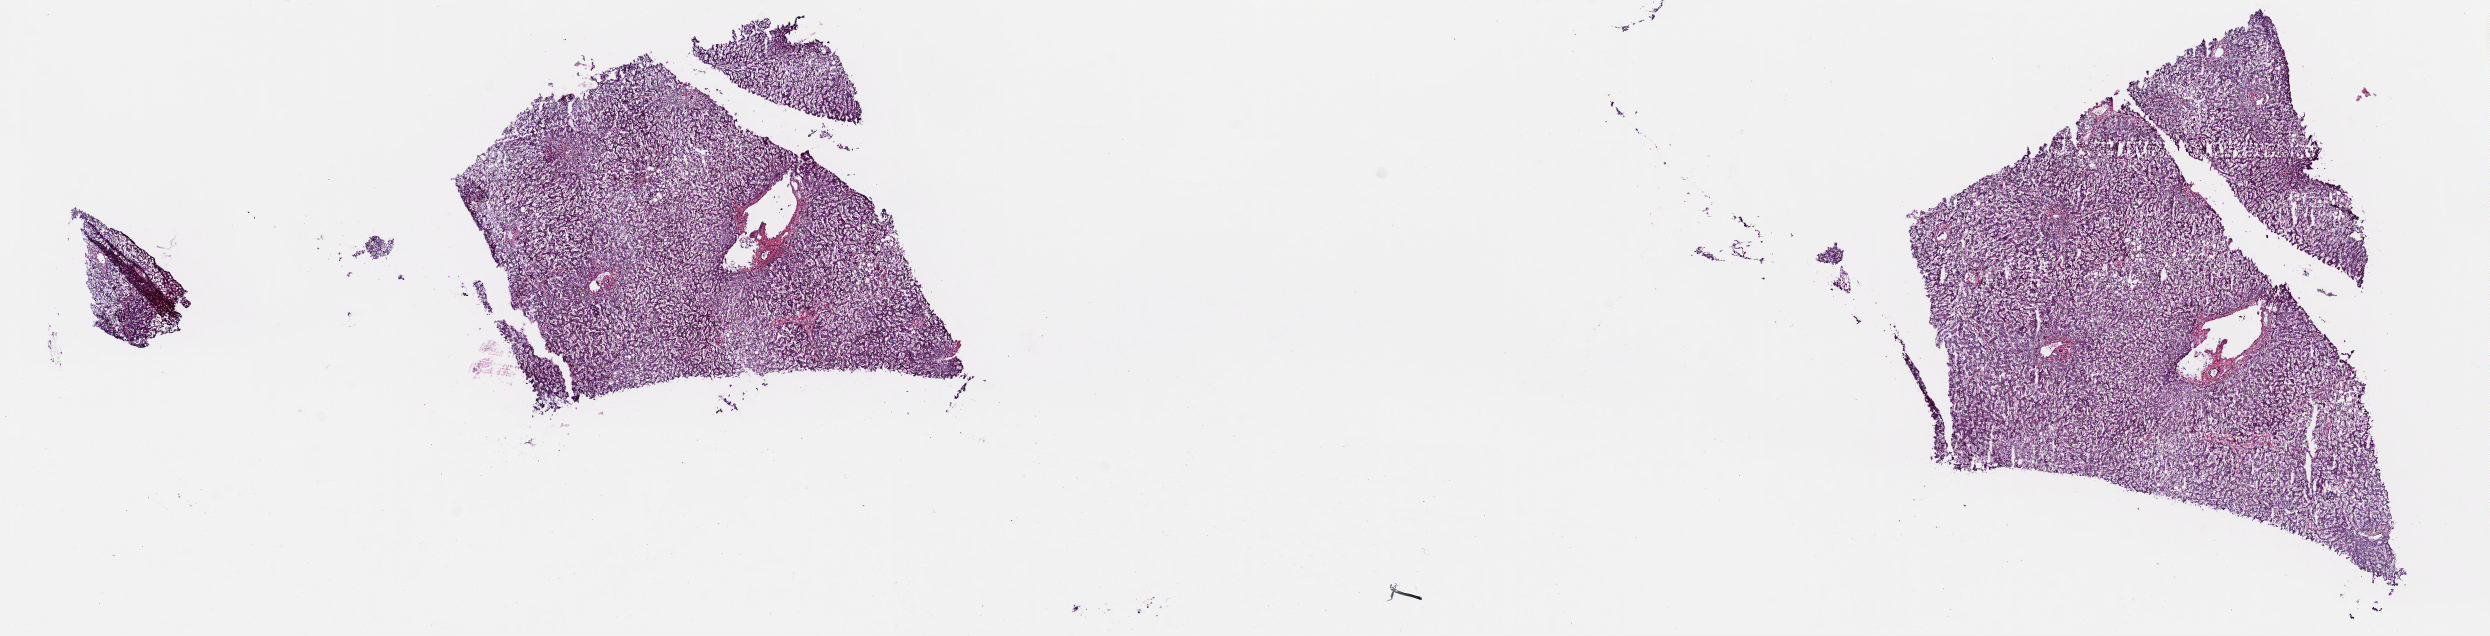
H&E whole-slide image — shown as a low-resolution overview of the whole scanned area (about 19.7 x 5.0 mm). Frozen section. Liver, solid tissue normal (non-tumour tissue) sample. Male, age 73 years at initial diagnosis. Composition of this section per pathologist review: tumour cells 0%, tumour nuclei 0%, normal cells 100%, stromal cells 0%, necrosis 0%. Infiltration values recorded for this section: lymphocyte infiltration 0%, monocyte infiltration 0%, neutrophil infiltration 0%.
- this section: solid tissue normal (non-tumour) sample from the same patient
- patient diagnosis: Hepatocellular carcinoma, NOS